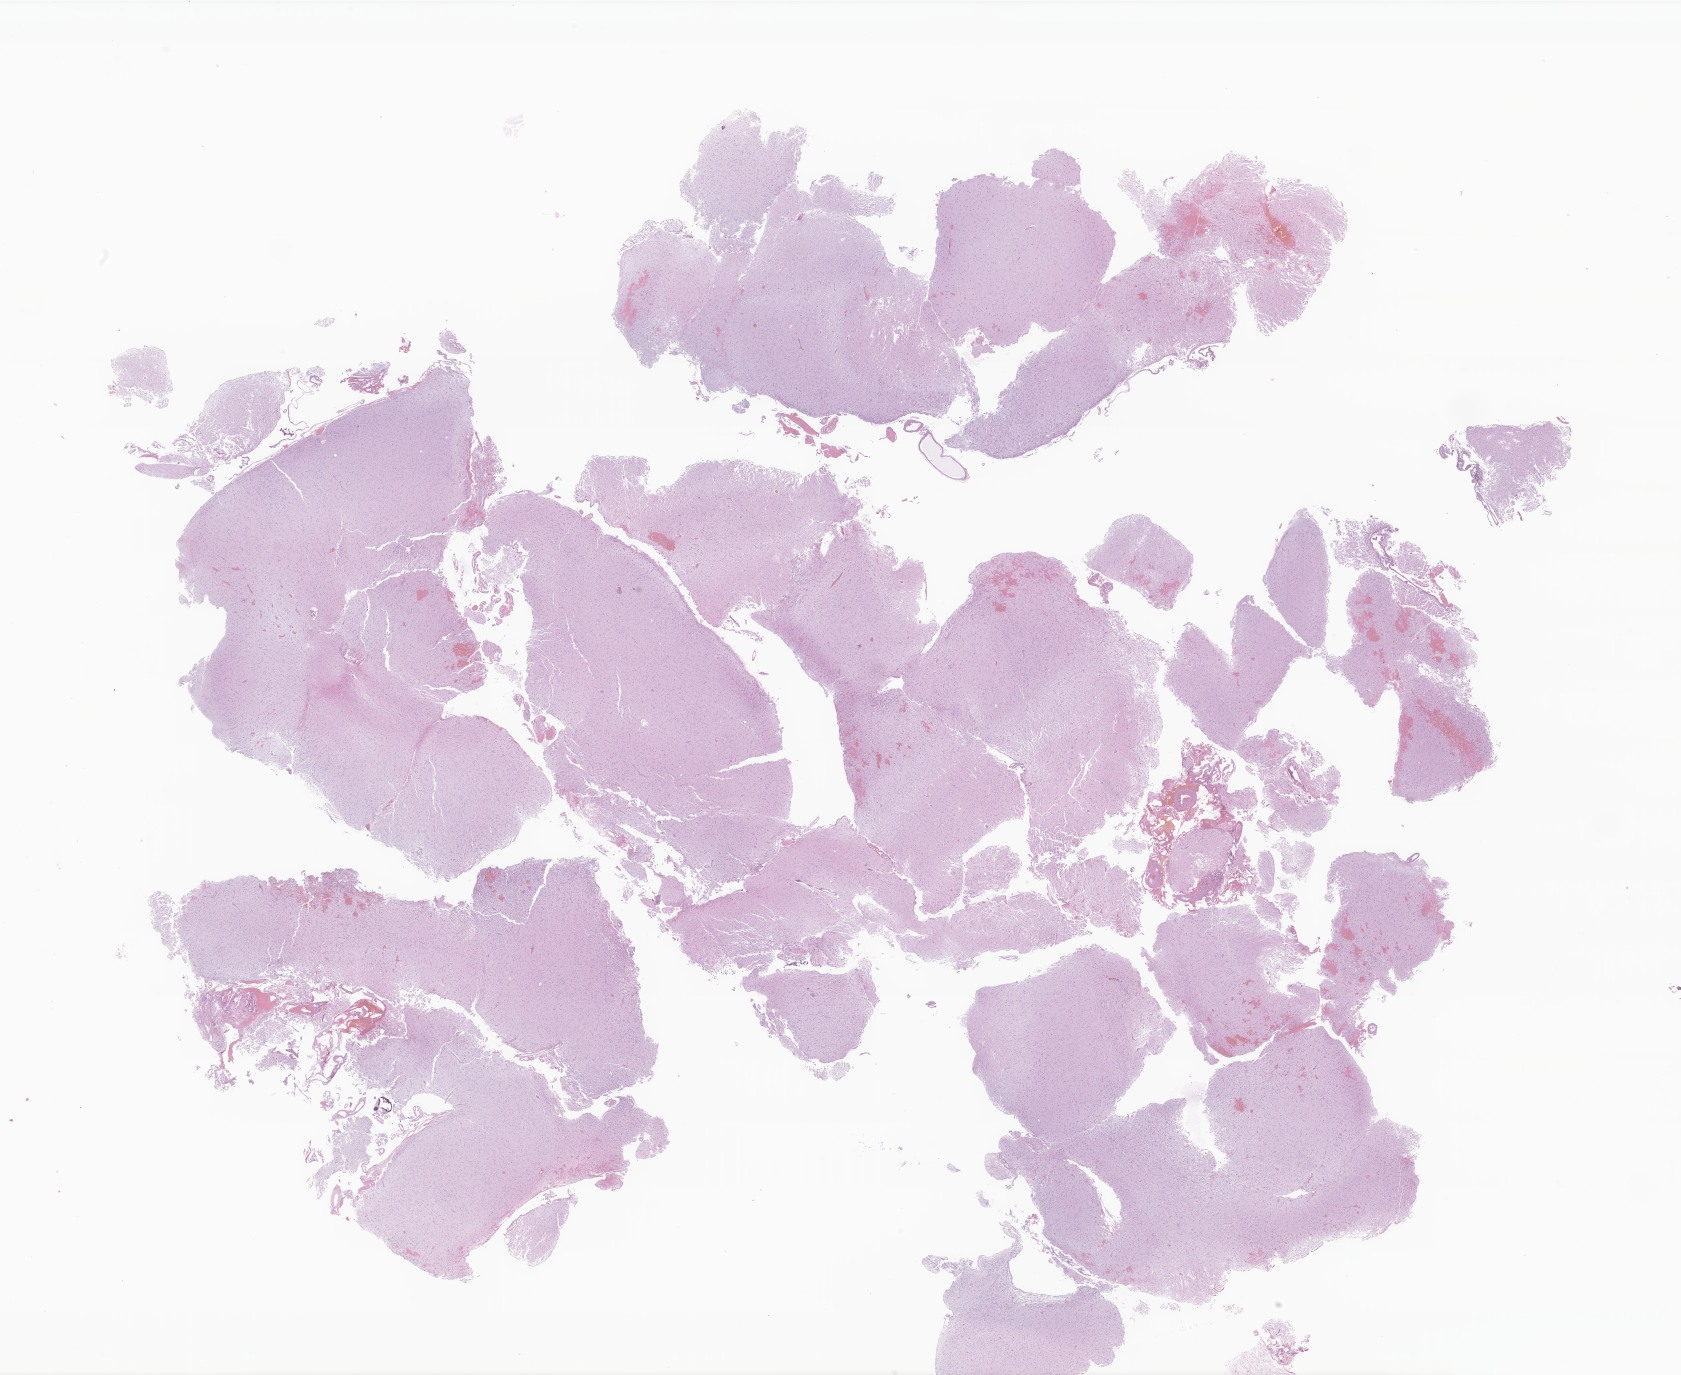
Digitized haematoxylin and eosin-stained section of tumor tissue from the brain — a low-resolution overview of the entire scanned area, about 28.3 x 23.2 mm. FFPE section. Male patient, age 218 months (18 years 2 months).
* diagnosis (ICD-O-3 morphology term): Neoplasm, uncertain whether benign or malignant